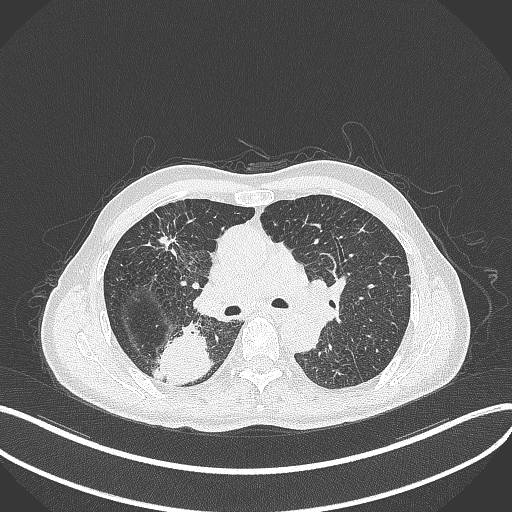
Chest CT, one axial slice. Position 277 of 428 along the scan axis. 120 kVp. Lung window (W 1500 / L -600 HU). 1 mm slice thickness. 512 × 512 image matrix, field of view 400 × 400 mm. Male patient, age 79 years. From the clinical record (not read from this slice): clinical TNM (as recorded): T3 N0 M0.
Annotated regions visible in this slice (rectangle marked by the reading radiologist):
- lung tumour (recorded histology: adenocarcinoma): bounding box [x1, y1, x2, y2] px = [161, 319, 210, 388]